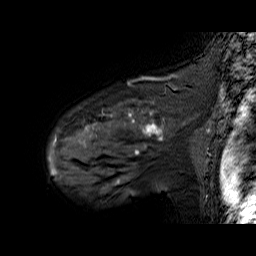
Breast MRI (dynamic contrast-enhanced), one sagittal slice. Position 50 of 60 along the scan axis. Dynamic contrast-enhanced series, time point 2 of 6 at this slice position (early post-contrast). 1.5 T. TE 6.3 ms, TR 32.9 ms. 4 mm slice thickness. 256 × 256 image matrix. Female patient. From the clinical record (not read from this slice): setting: breast cancer imaged before/during neoadjuvant chemotherapy; receptor status: HER2-positive.
Structures marked on this image (semi-automatically segmented with operator editing):
- analysis volume of interest (the breast-tissue region the enhancement analysis was run in; not a lesion): box from (x=48, y=92) to (x=195, y=174) px
- tumour enhancement mask (voxels above the 100 % enhancement threshold inside the analysis volume of interest): (x=48, y=111)–(x=163, y=174)